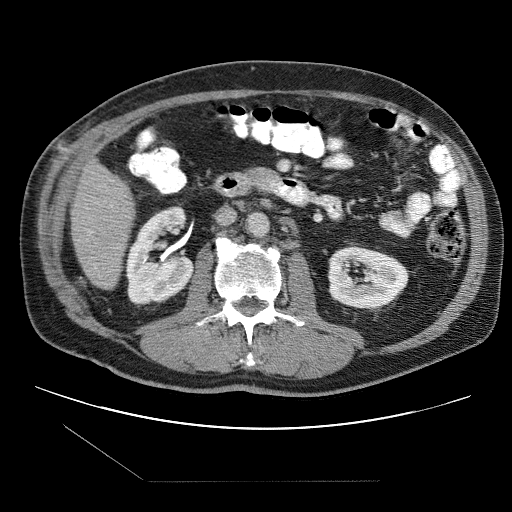
Contrast-enhanced abdominal CT (liver protocol), one axial slice. Slice 24 of 109 in the series (ordered by position). One of 2 acquisitions stored at this slice position. Soft-tissue window (W 400 / L 40 HU). 512 × 512 image matrix, field of view 400 × 400 mm. From the clinical record (not read from this slice): diagnosis: hepatocellular carcinoma (patient treated with transarterial chemoembolisation; whether this scan precedes or follows treatment is not stated here); TNM stage (as recorded): Stage-IIIB; Child-Pugh class: A; tumour differentiation: well differentiated; tumour nodularity: multinodular.
Structures marked on this image (semi-automatically segmented with operator editing):
- liver parenchyma outside the tumour (the mass and vessels are separate outlines, so this box may not span the whole liver): bounding box (x1, y1, x2, y2) in pixels: (70, 160, 134, 288)